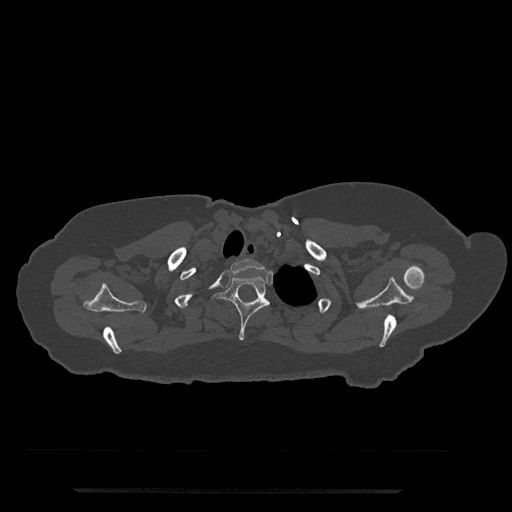
CT including the spine, one axial slice; position 676 of 797 along the scan axis; reconstruction kernel Br40s/3; bone window (W 1800 / L 400 HU); 0.5 mm slice thickness; 512 × 512 image matrix. Patient: female, 51 years. Case-level facts recorded for this patient, not image findings: primary cancer: neuro; vertebrae with lytic lesions (as recorded): T8.
Annotated regions visible in this slice (semi-automatic segmentation, software-assisted and operator-edited):
- T1 vertebra: bounding box (x1, y1, x2, y2) in pixels: (230, 259, 265, 273)
- T2 vertebra: (213, 275, 270, 341)